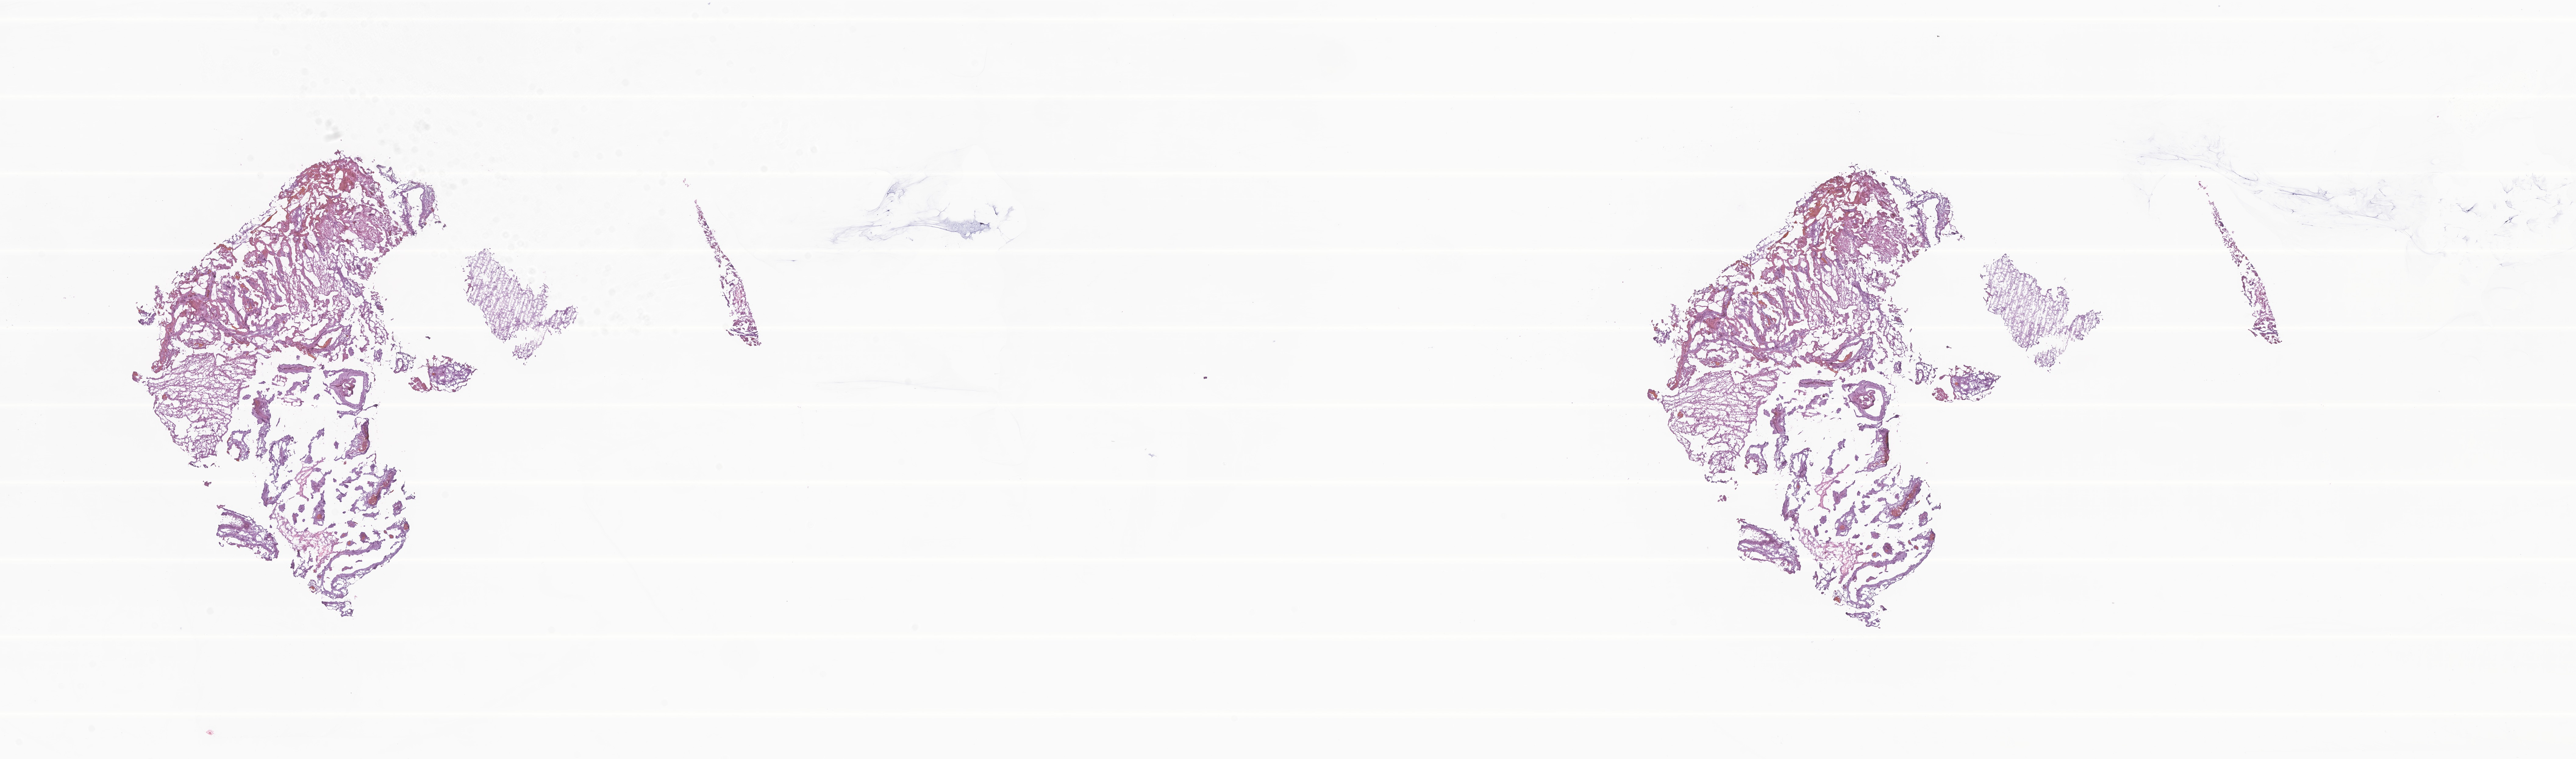
Hematoxylin and eosin (H&E) whole-slide image of tumor tissue from the brain, a low-resolution overview of the entire scanned area, about 35.6 x 10.5 mm. Cryosection (OCT / tissue freezing medium). Patient male; age 54 months (4 years 6 months).
Recorded diagnosis: Astrocytoma, NOS.